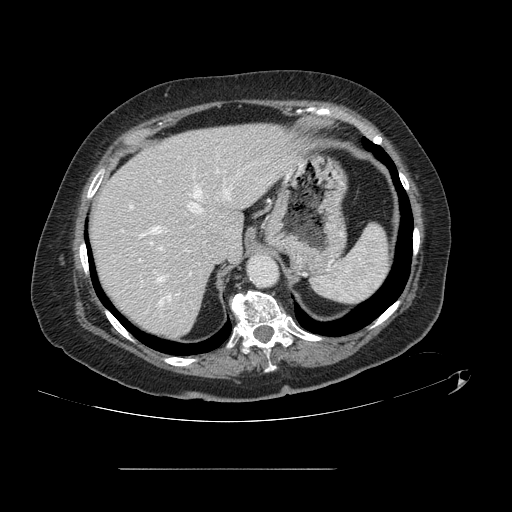
Contrast-enhanced abdominal CT, one axial slice. Position 103 of 148 along the scan axis. Intravenous contrast given. Soft-tissue window (W 400 / L 40 HU). 512 × 512 image matrix. Female patient, age 75 years. Case-level facts recorded for this patient, not image findings: diagnosis: colorectal cancer liver metastases, imaged before liver resection; multiple liver metastases: no; largest metastasis: 2.4 cm; chemotherapy before resection: no.
Structures marked on this image (manually delineated by an expert):
- hepatic veins: bounding box [x1, y1, x2, y2] px = [141, 169, 233, 305]
- liver: [90, 124, 300, 338]
- planned liver remnant (the part of the liver to remain after resection): [90, 124, 297, 338]
- portal vein (with intrahepatic branches): [130, 205, 163, 250]